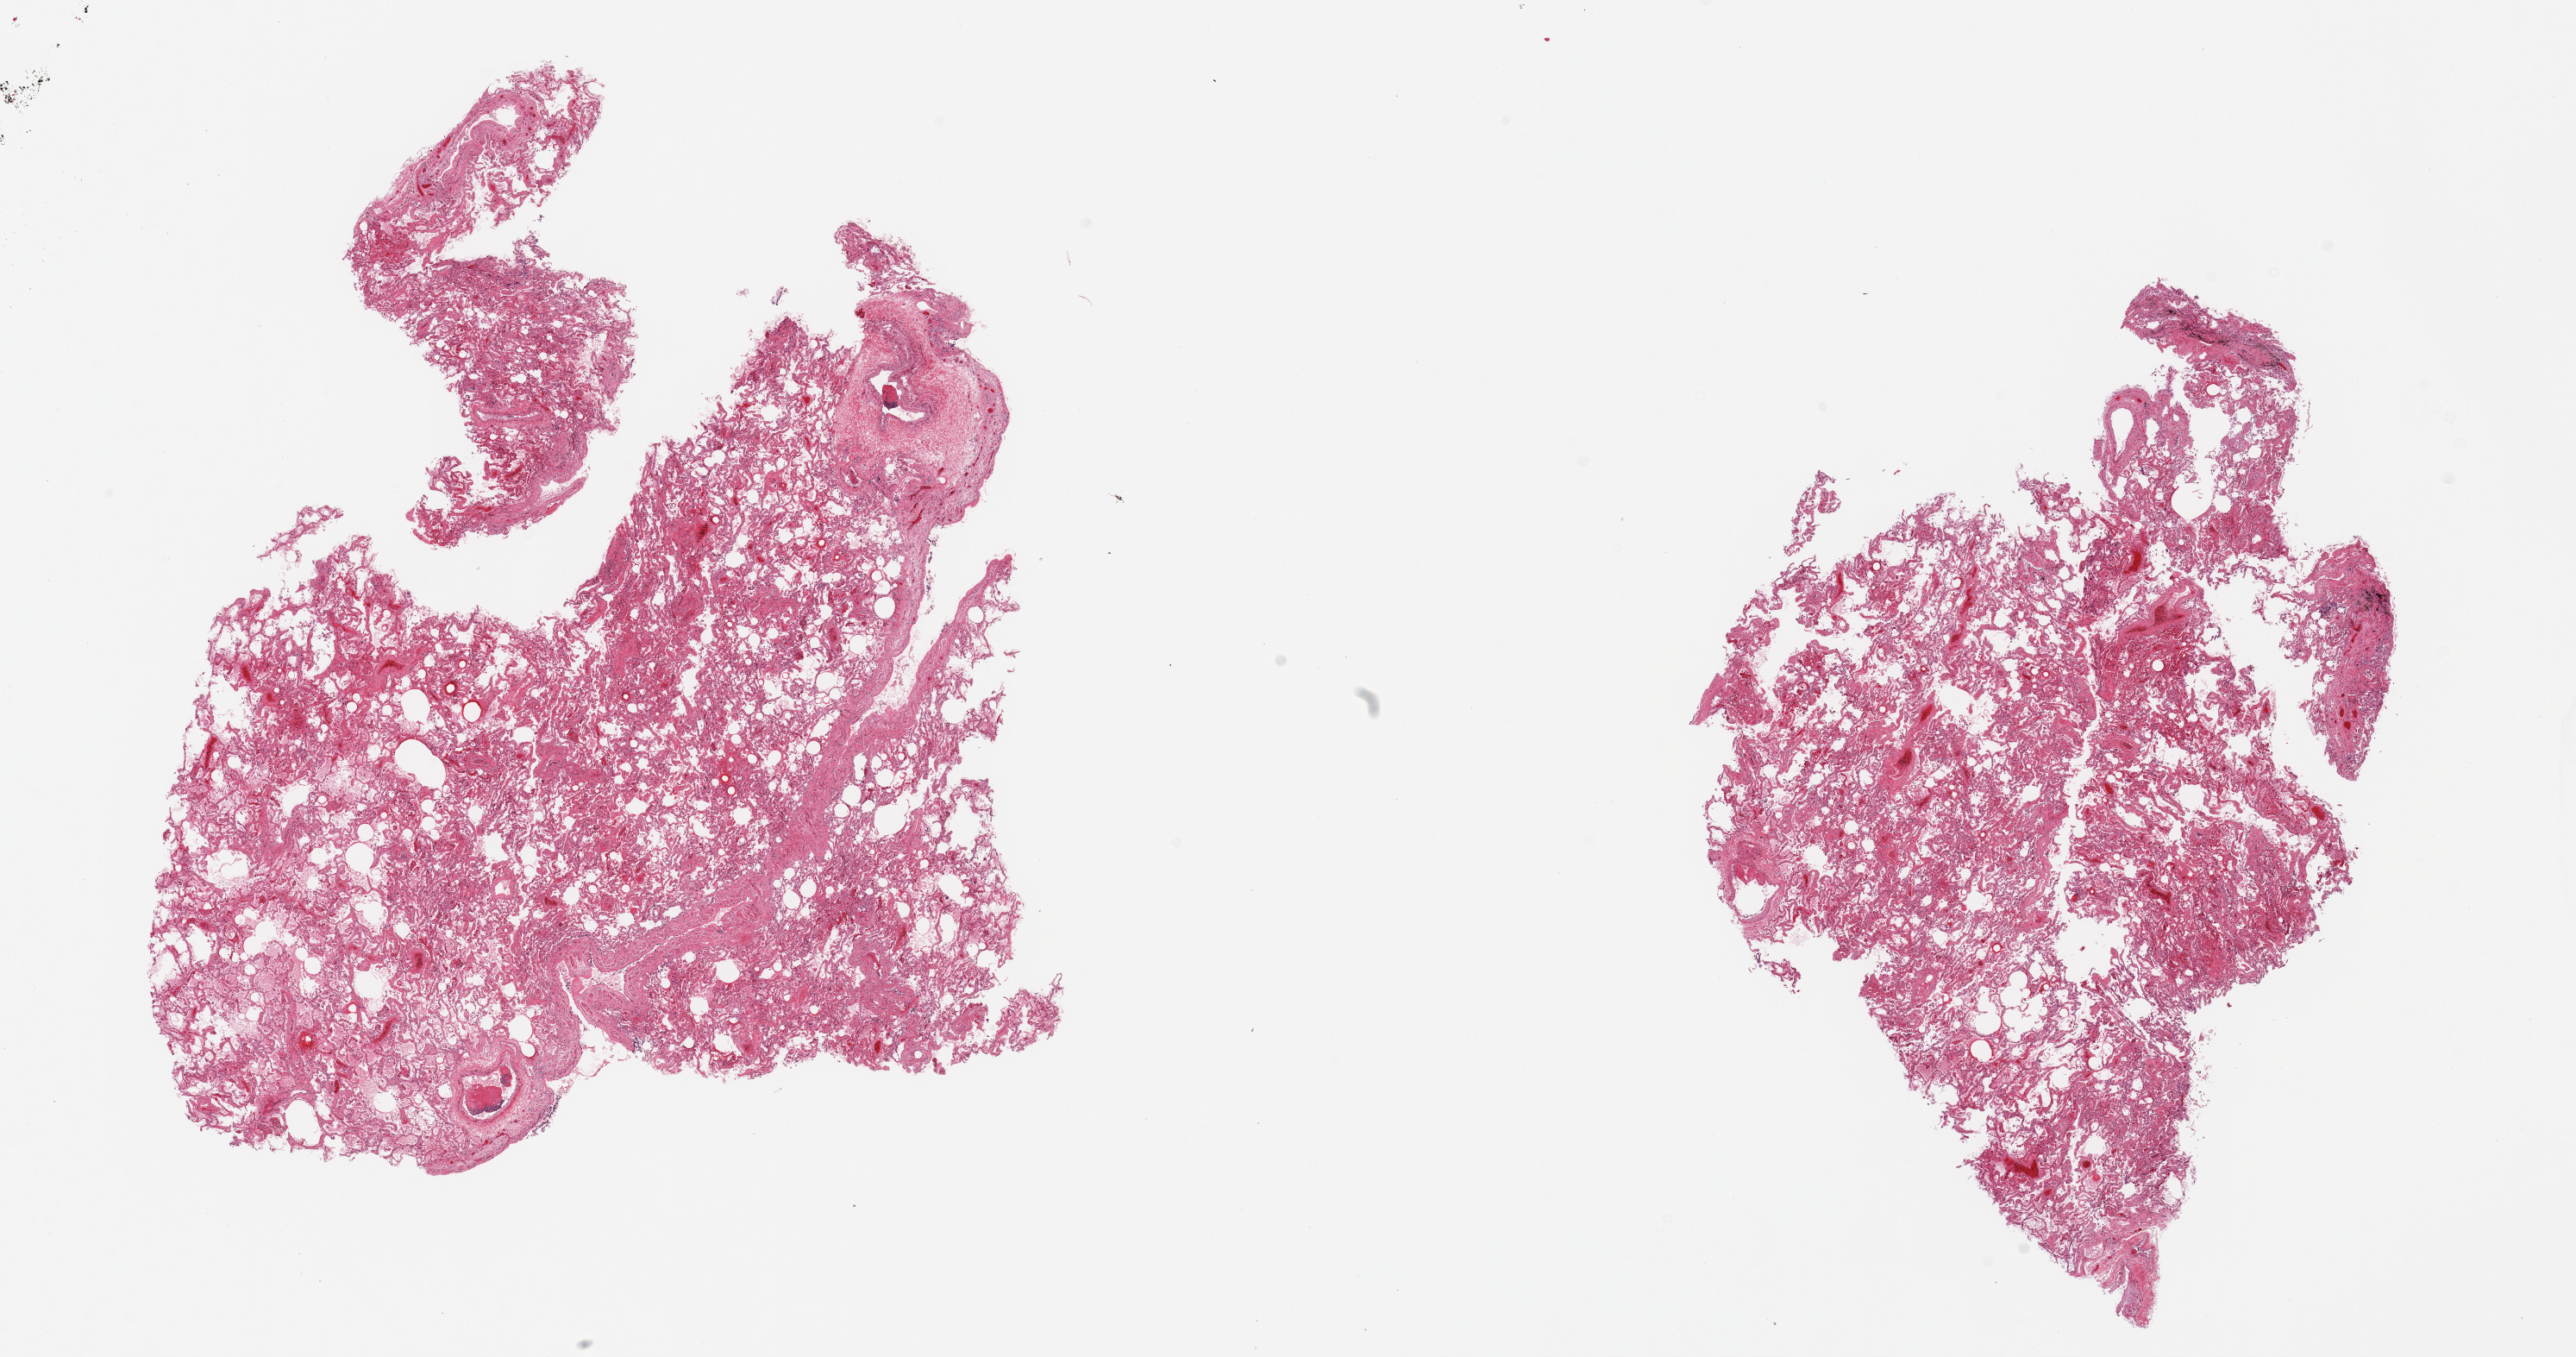
Whole-slide image, haematoxylin and eosin stain, a low-resolution overview of the entire scanned area, about 23.6 x 12.4 mm; PAXgene-fixed paraffin-embedded (PFPE) section; target tissue: lung; tissue donor sample. Donor sex: female.
Reviewer comment on this tissue sample: 2 pieces; congested with small focal hemorrhages.